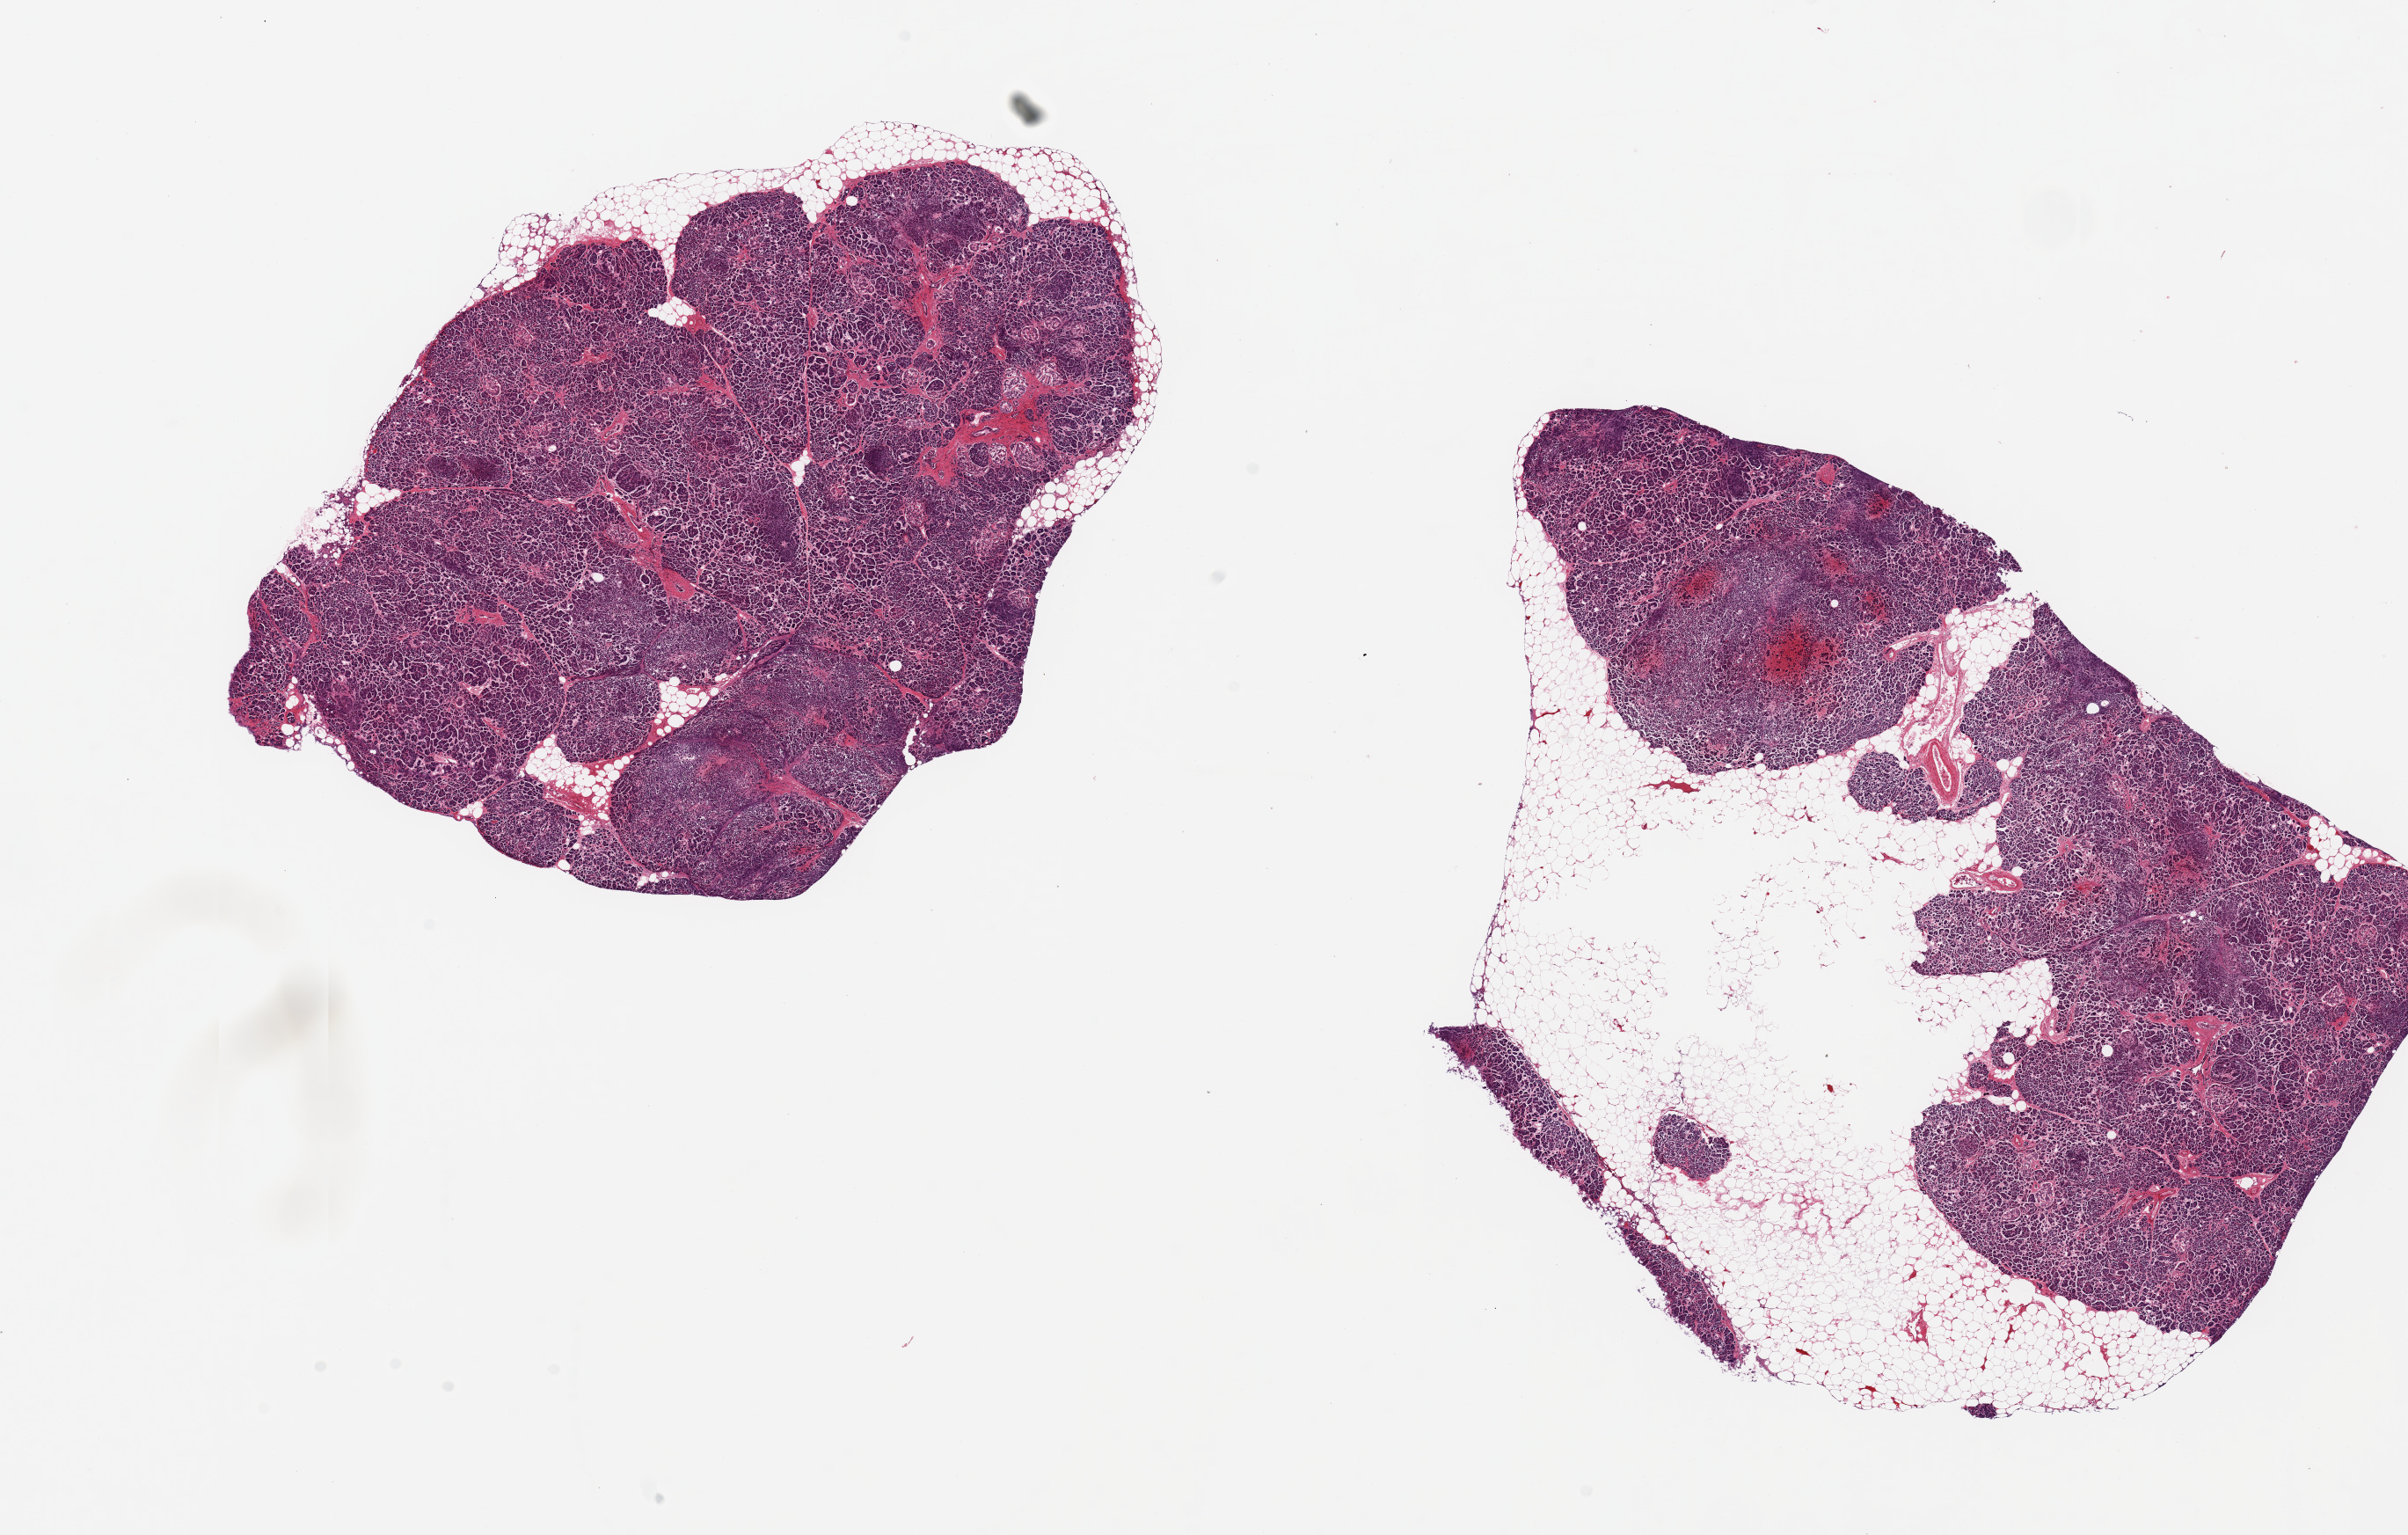
Digitized H&E-stained section, whole scanned area (about 21.7 x 13.8 mm, acquisition: 20x scan) shown as a low-resolution overview. PAXgene-fixed paraffin-embedded (PFPE) section. Section of pancreas (target tissue). Tissue donor sample. Donor: male.
Review note (as recorded): 2 pieces,~9.6x7mm w/50% fat; 5.6x7.7mm w/10% fat.